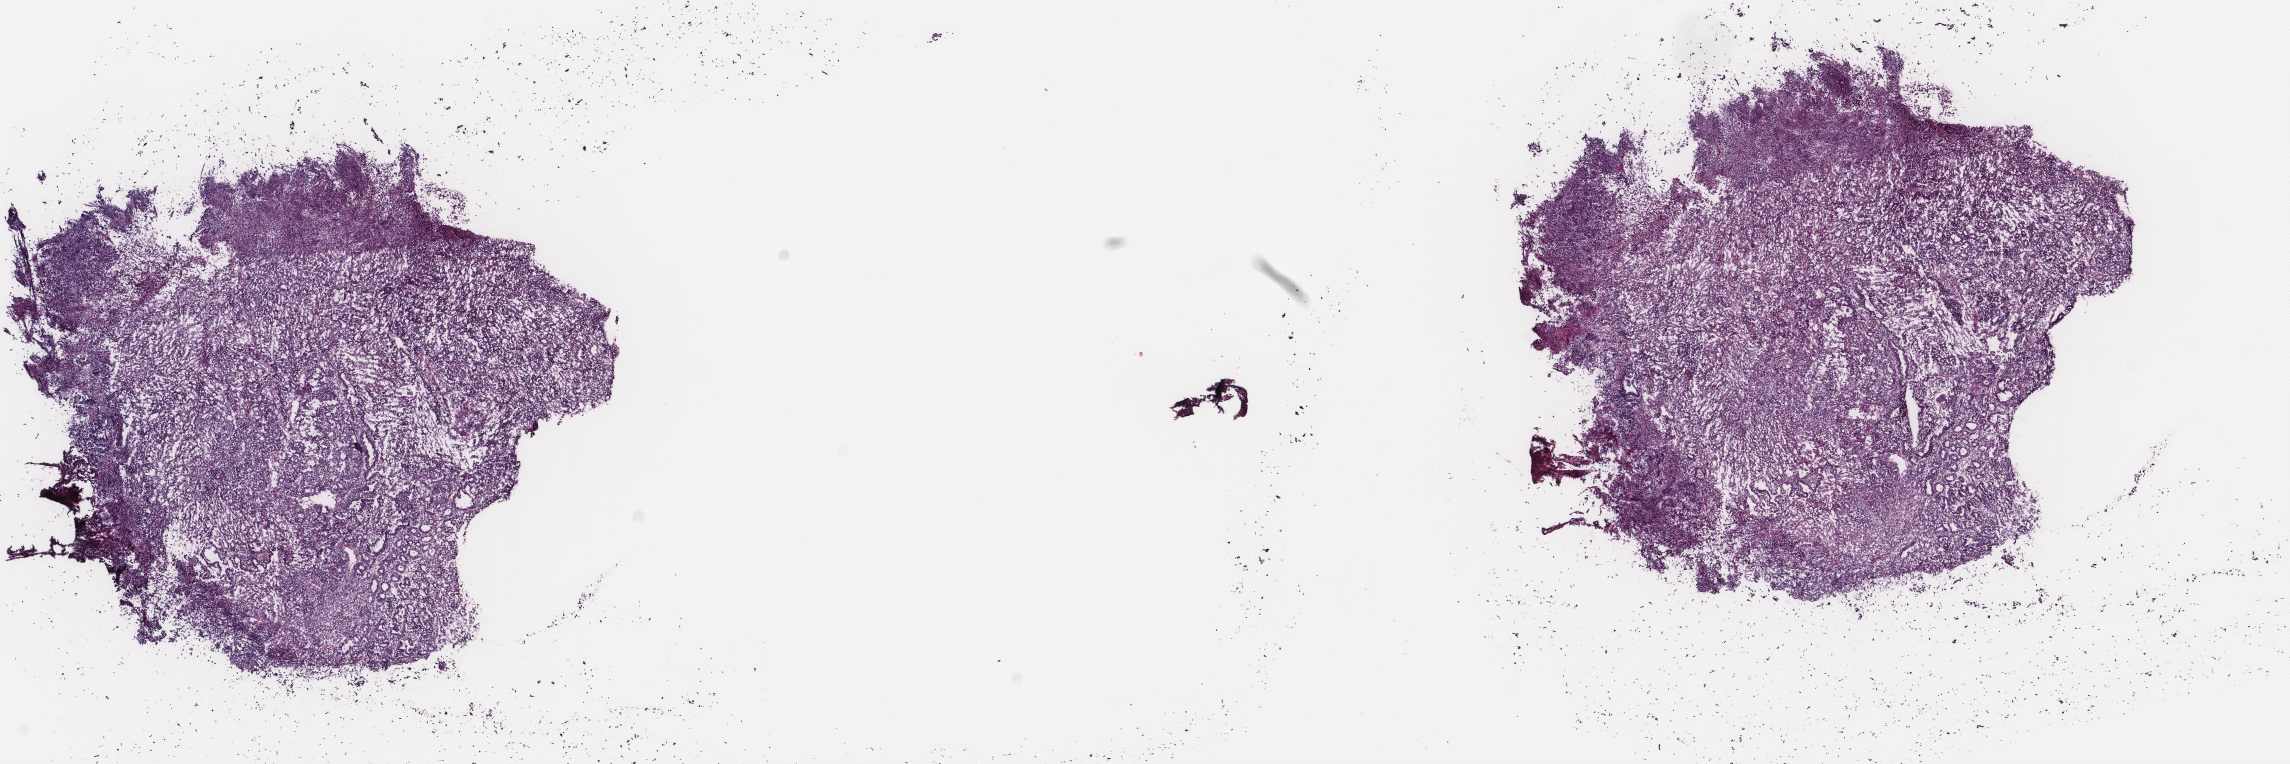
Whole-slide histology image, H&E — whole scanned area (about 18.2 x 6.1 mm, from a 40x scan) shown as a low-resolution overview; frozen section from the top of the tissue portion; uterus, primary tumour sample. Female patient. Histologic grade: G3 (poorly differentiated). Slide review estimates, as recorded: tumour cells 90%, tumour nuclei 90%, normal cells 0%, stromal cells 10%, necrosis 0%. Inflammatory infiltration, as recorded: lymphocyte infiltration 20%, monocyte infiltration 6%, neutrophil infiltration 3%.
• diagnosis: Endometrioid adenocarcinoma, NOS (endometrium)
• FIGO stage: IC